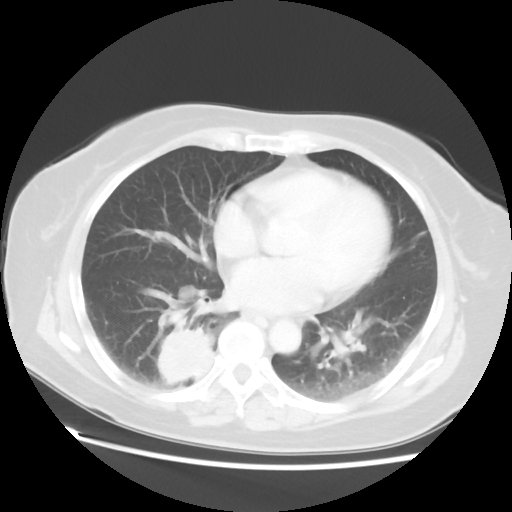
Chest CT, one axial slice; reconstruction kernel STANDARD; lung window (W 1500 / L -600 HU); 512 × 512 image matrix, field of view 356 × 356 mm. Patient: female, 69 years. Case-level facts recorded for this patient, not image findings: clinical TNM (as recorded): T2 N1 M1a.
Structures marked on this image (bounding box drawn by a radiologist):
- lung tumour (recorded histology: adenocarcinoma): bounding box (x1, y1, x2, y2) in pixels: (154, 324, 218, 391)